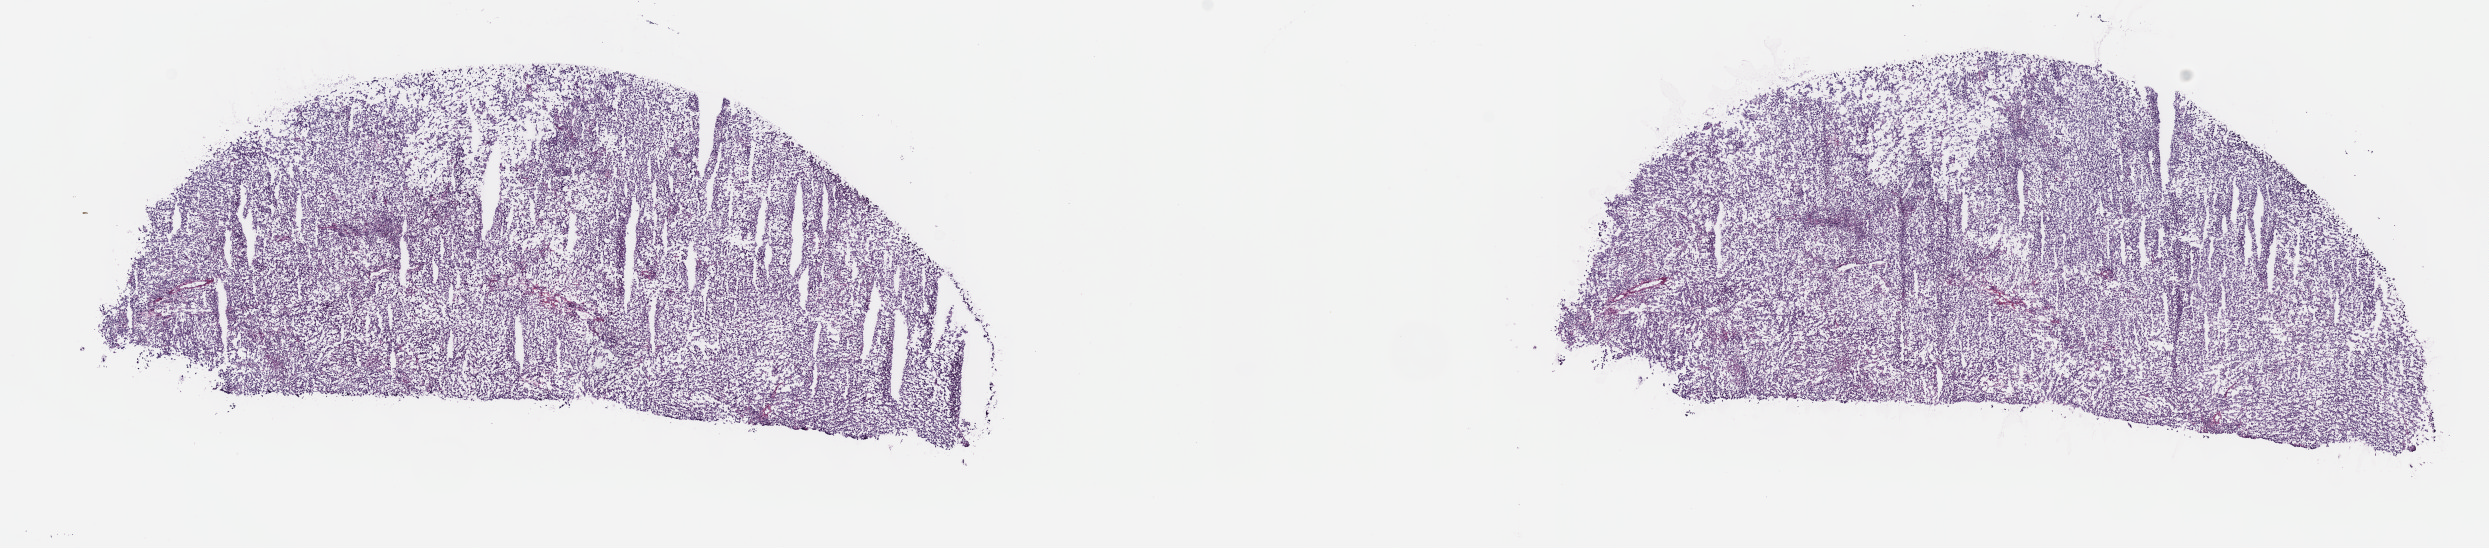
Digitized Hematoxylin and eosin (H&E) stained tissue section (whole slide) — shown as a low-resolution overview of the whole scanned area (about 20.1 x 4.4 mm), frozen section from the top of the tissue portion, sample: primary tumour, testis. Male patient; age at initial diagnosis 20 years. Slide review estimates, as recorded: tumour cells 60%, tumour nuclei 60%, normal cells 0%, stromal cells 30%, necrosis 10%. Infiltration values recorded for this section: lymphocyte infiltration 0%, monocyte infiltration 0%, neutrophil infiltration 0%.
AJCC pathologic stage: I (7th edition). TNM: T1 NX. Histologic diagnosis: Seminoma, NOS.